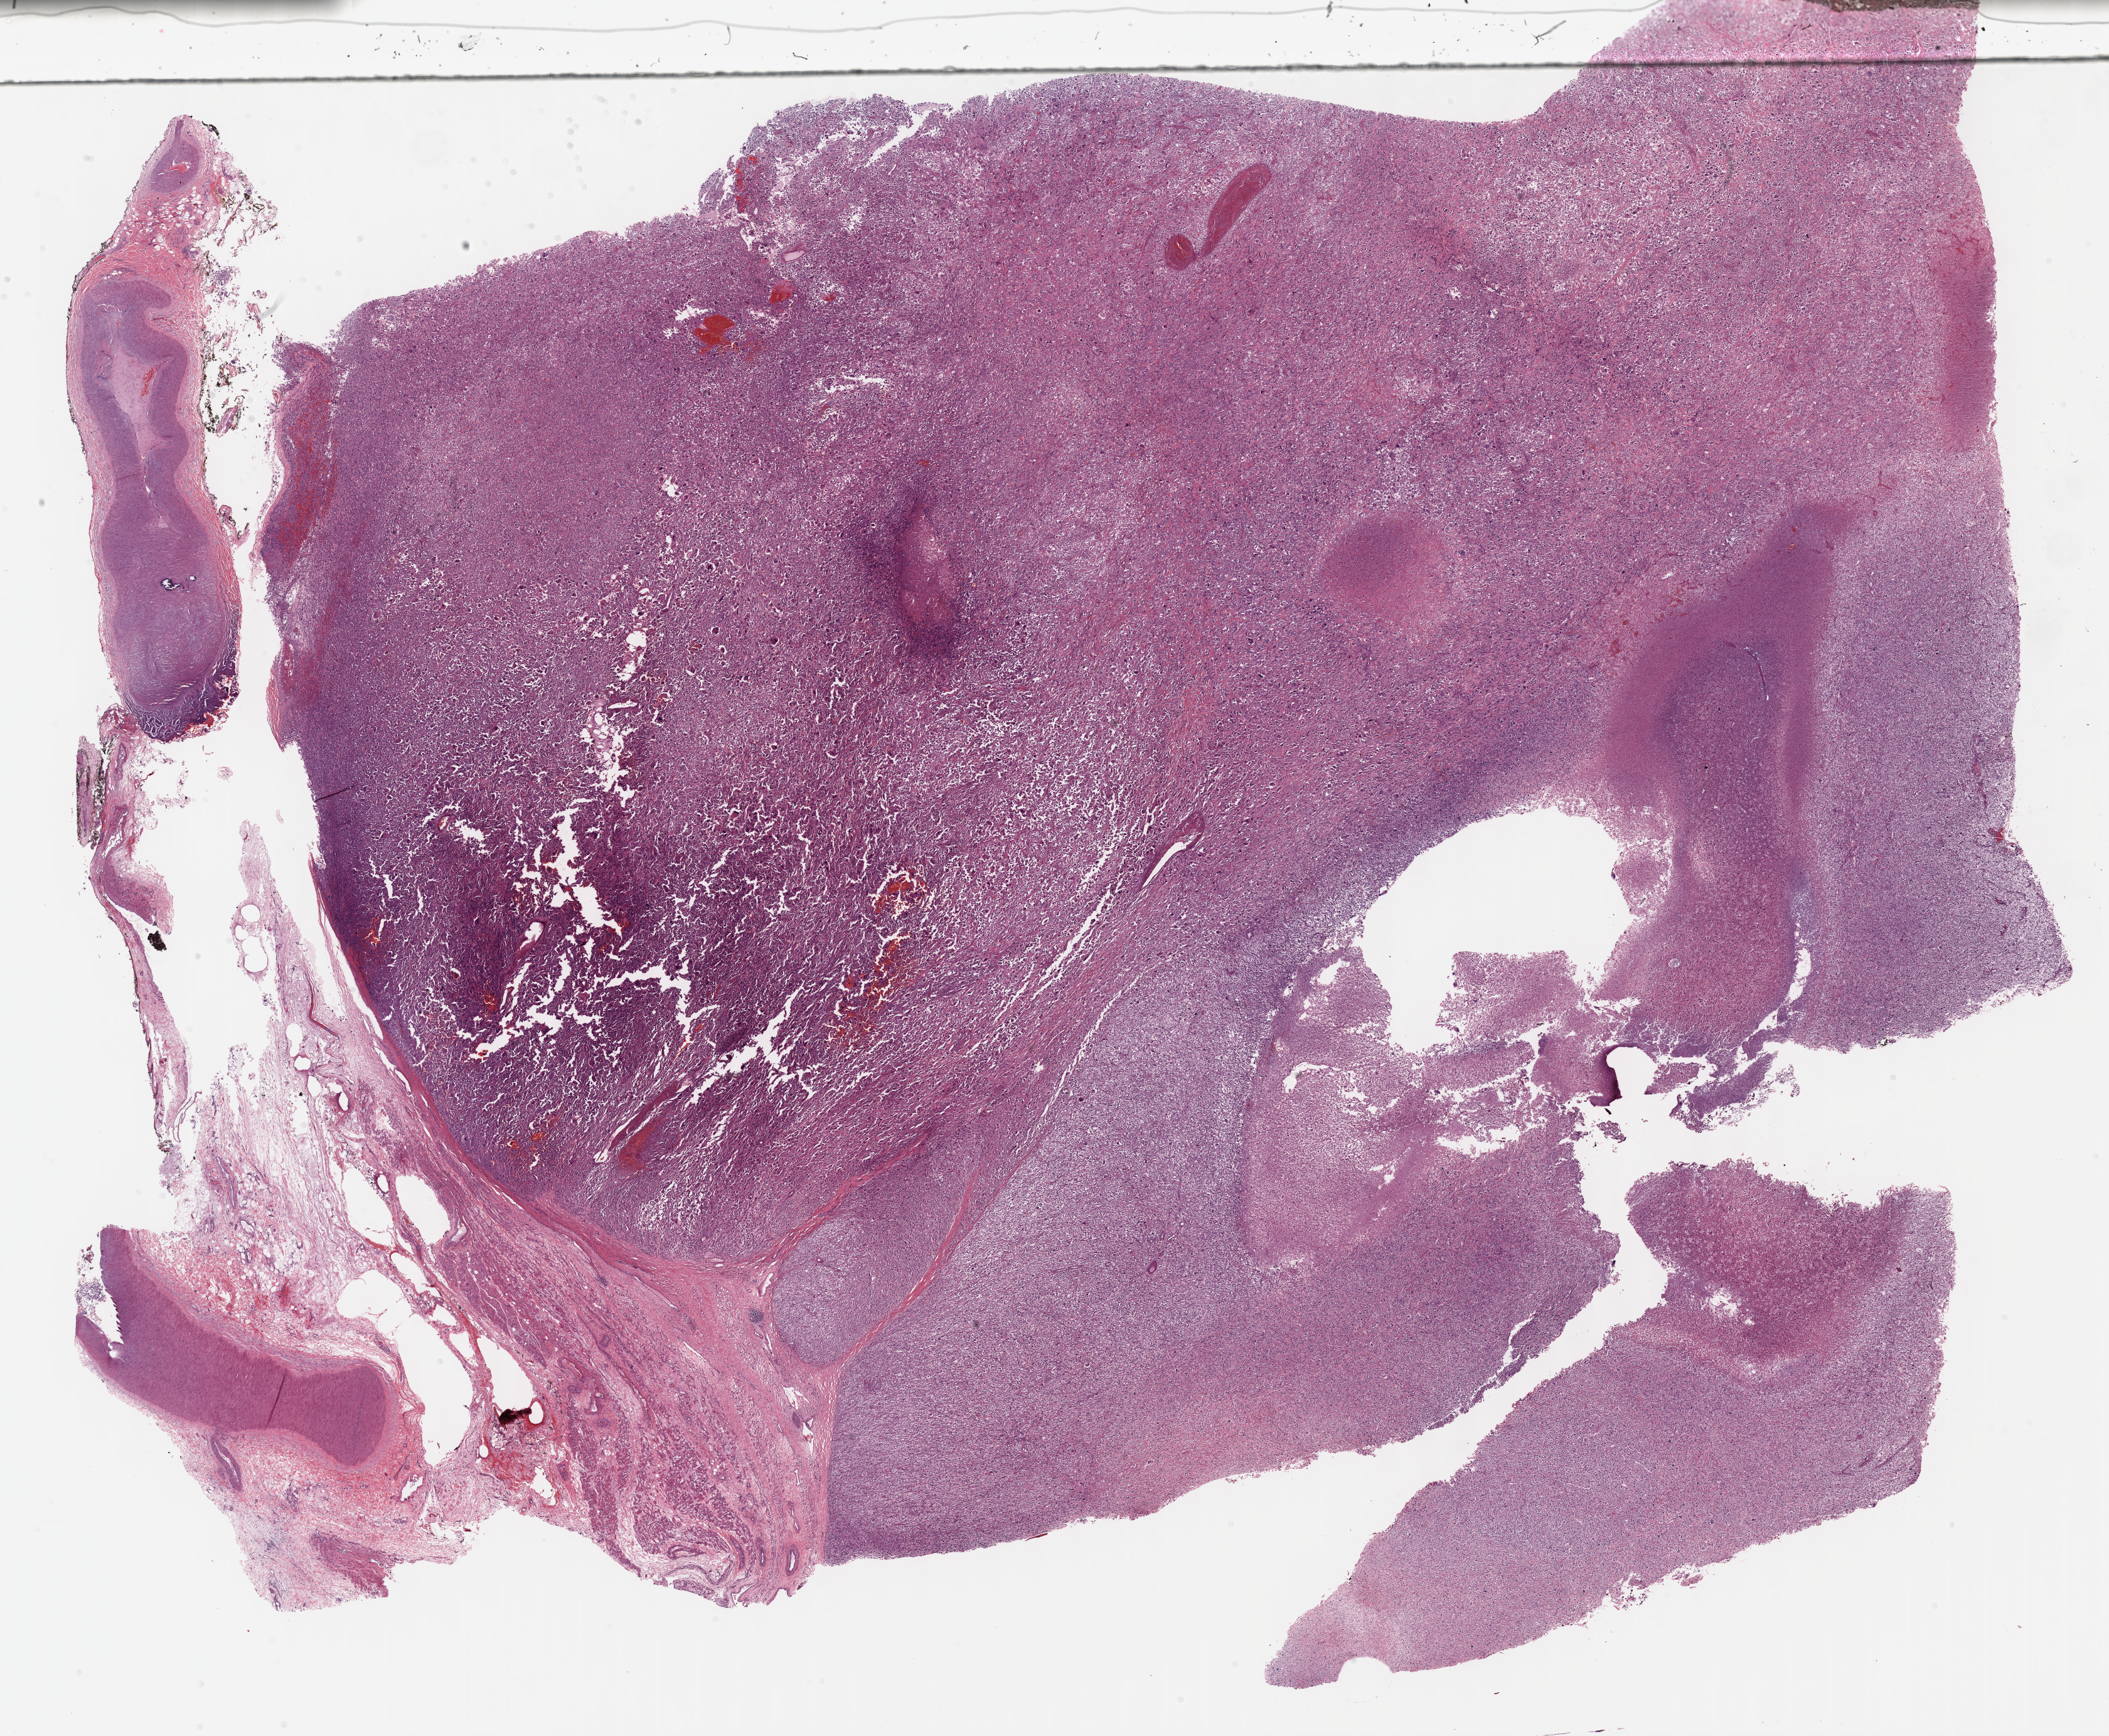
Digitized H&E-stained tissue section (whole slide) — a low-resolution overview of the entire scanned area, about 27.2 x 22.4 mm (slide scanned at 40x). Formalin-fixed paraffin-embedded (FFPE) diagnostic section. Primary tumour sample from the connective, subcutaneous and other soft tissues. Female, age 68 years at initial diagnosis.
Diagnosis: Undifferentiated sarcoma (connective, subcutaneous and other soft tissues of lower limb and hip).